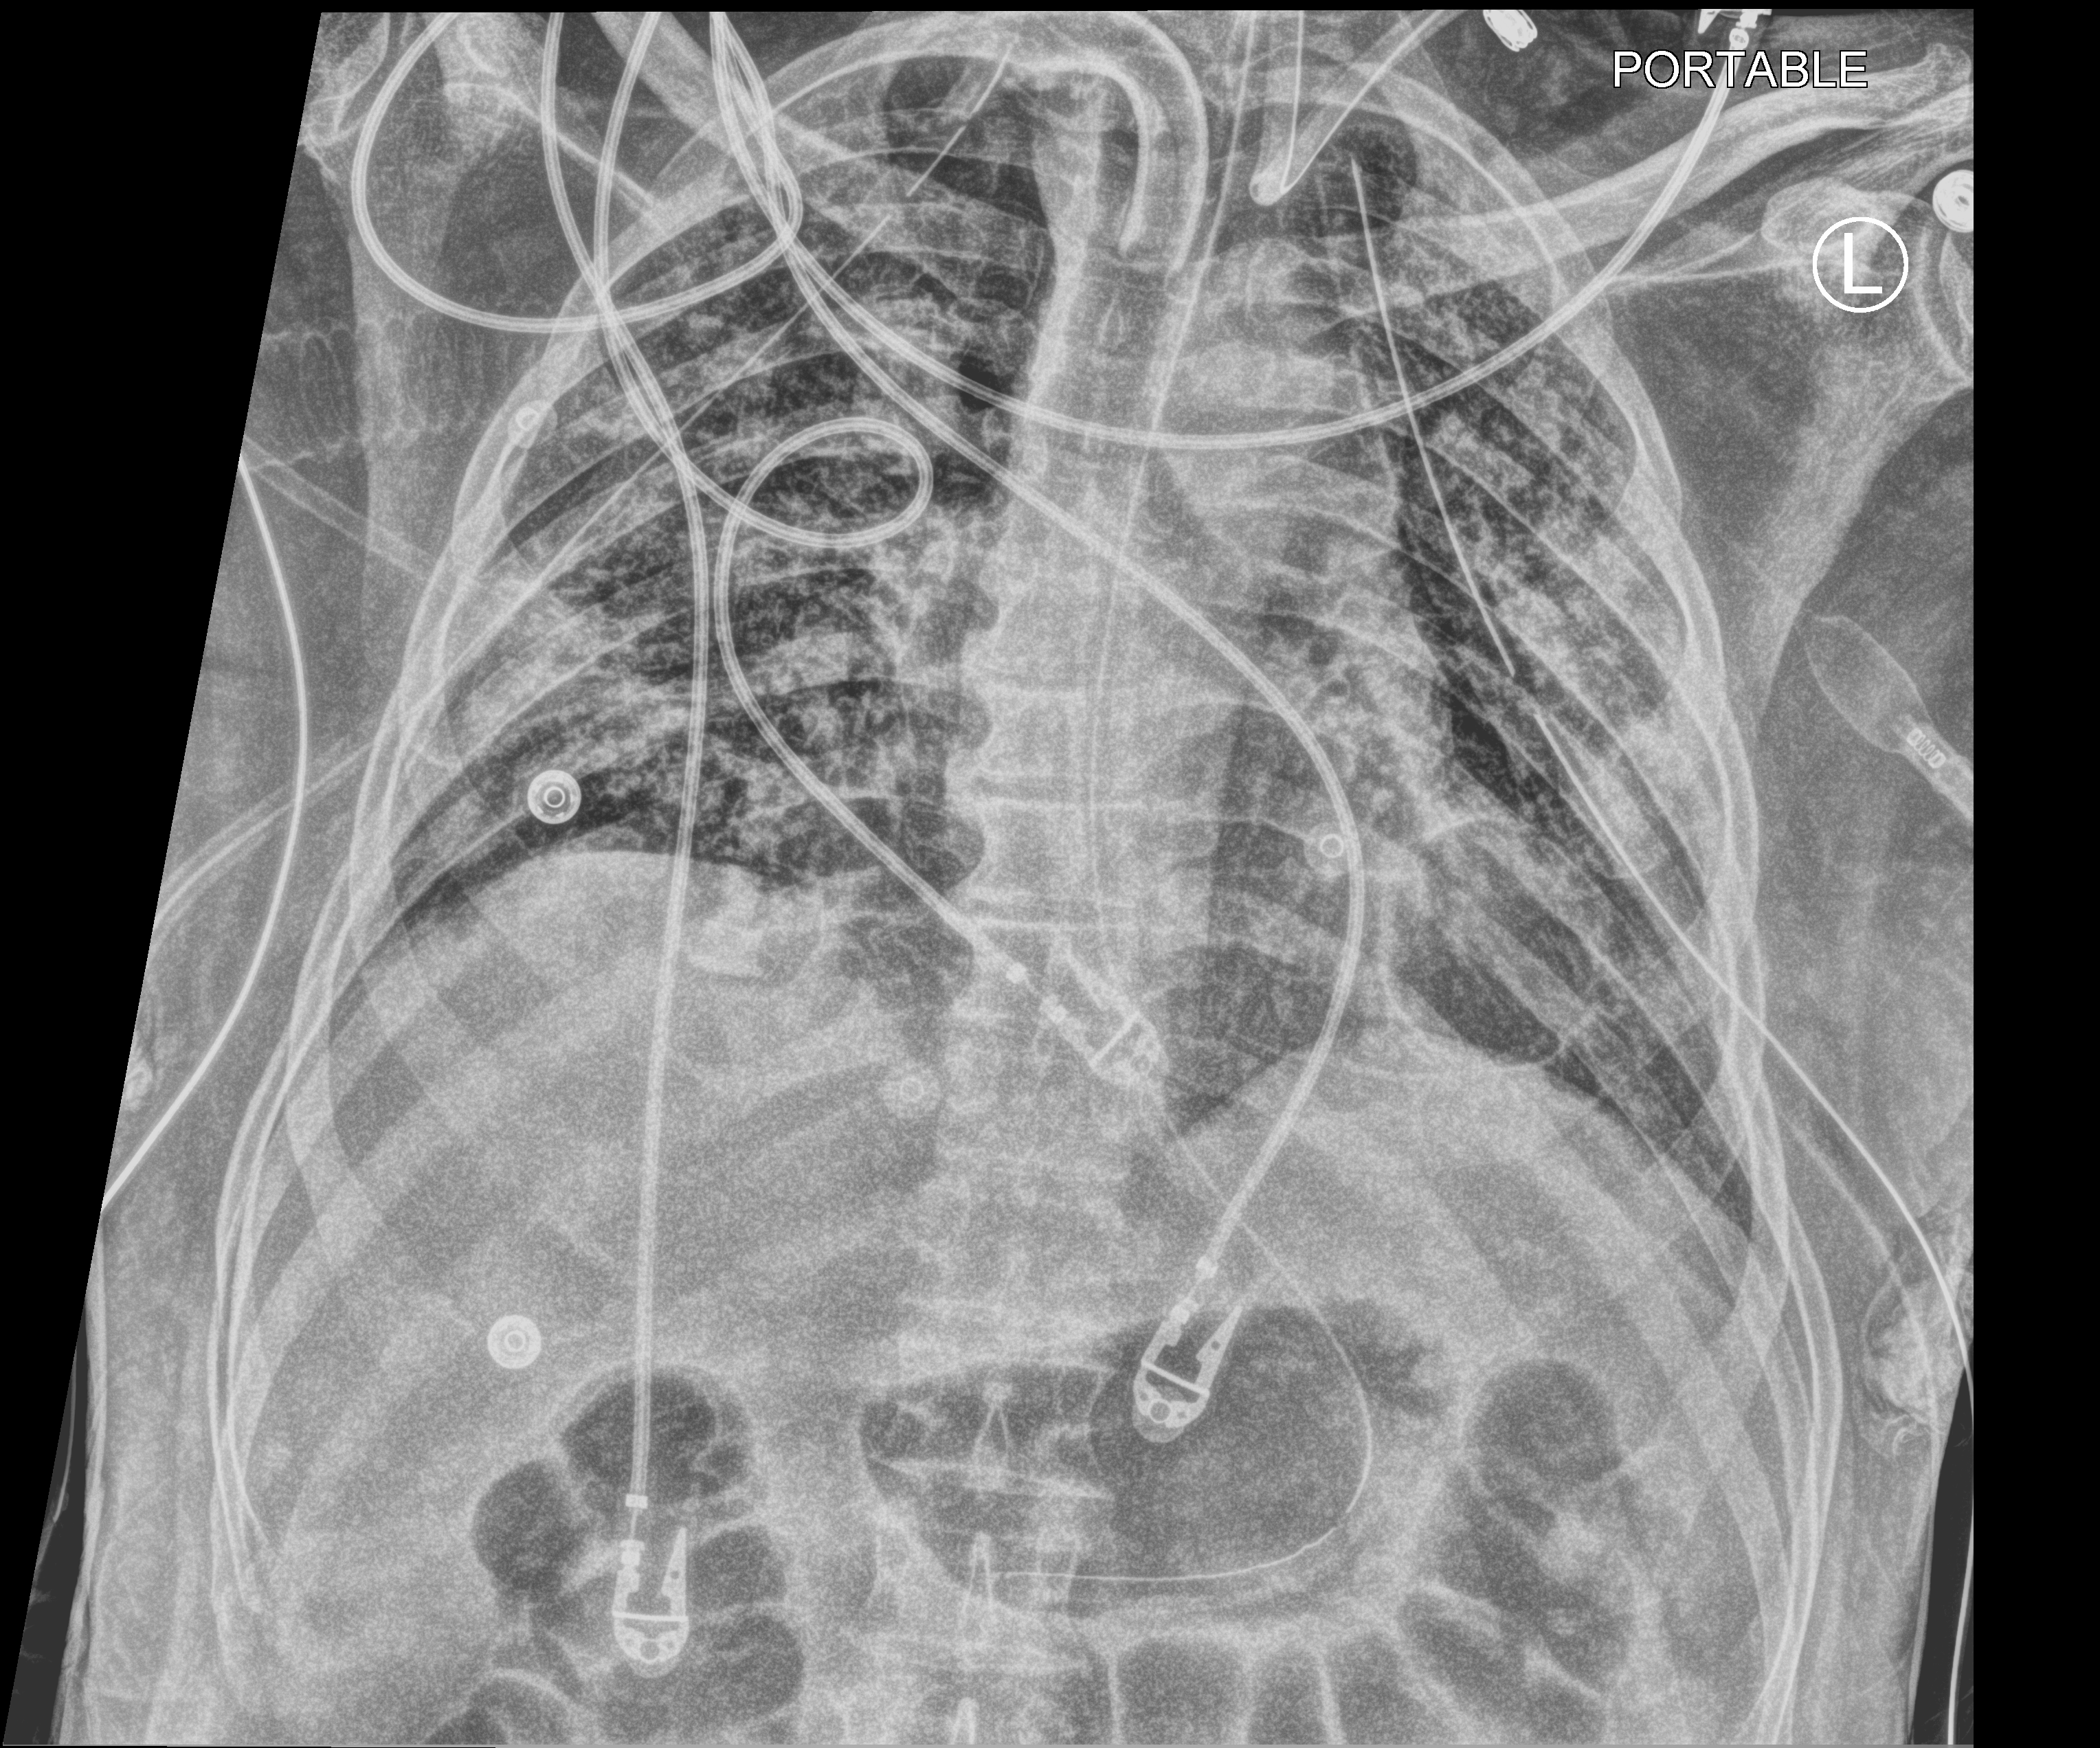
Portable chest radiograph, anteroposterior (AP) projection. Patient hospitalised with COVID-19; male, aged 18–59 years.
Hospital-stay facts (about this admission, not read from this image; timing relative to this image not recorded):
- admitted to intensive care during this hospital stay: yes